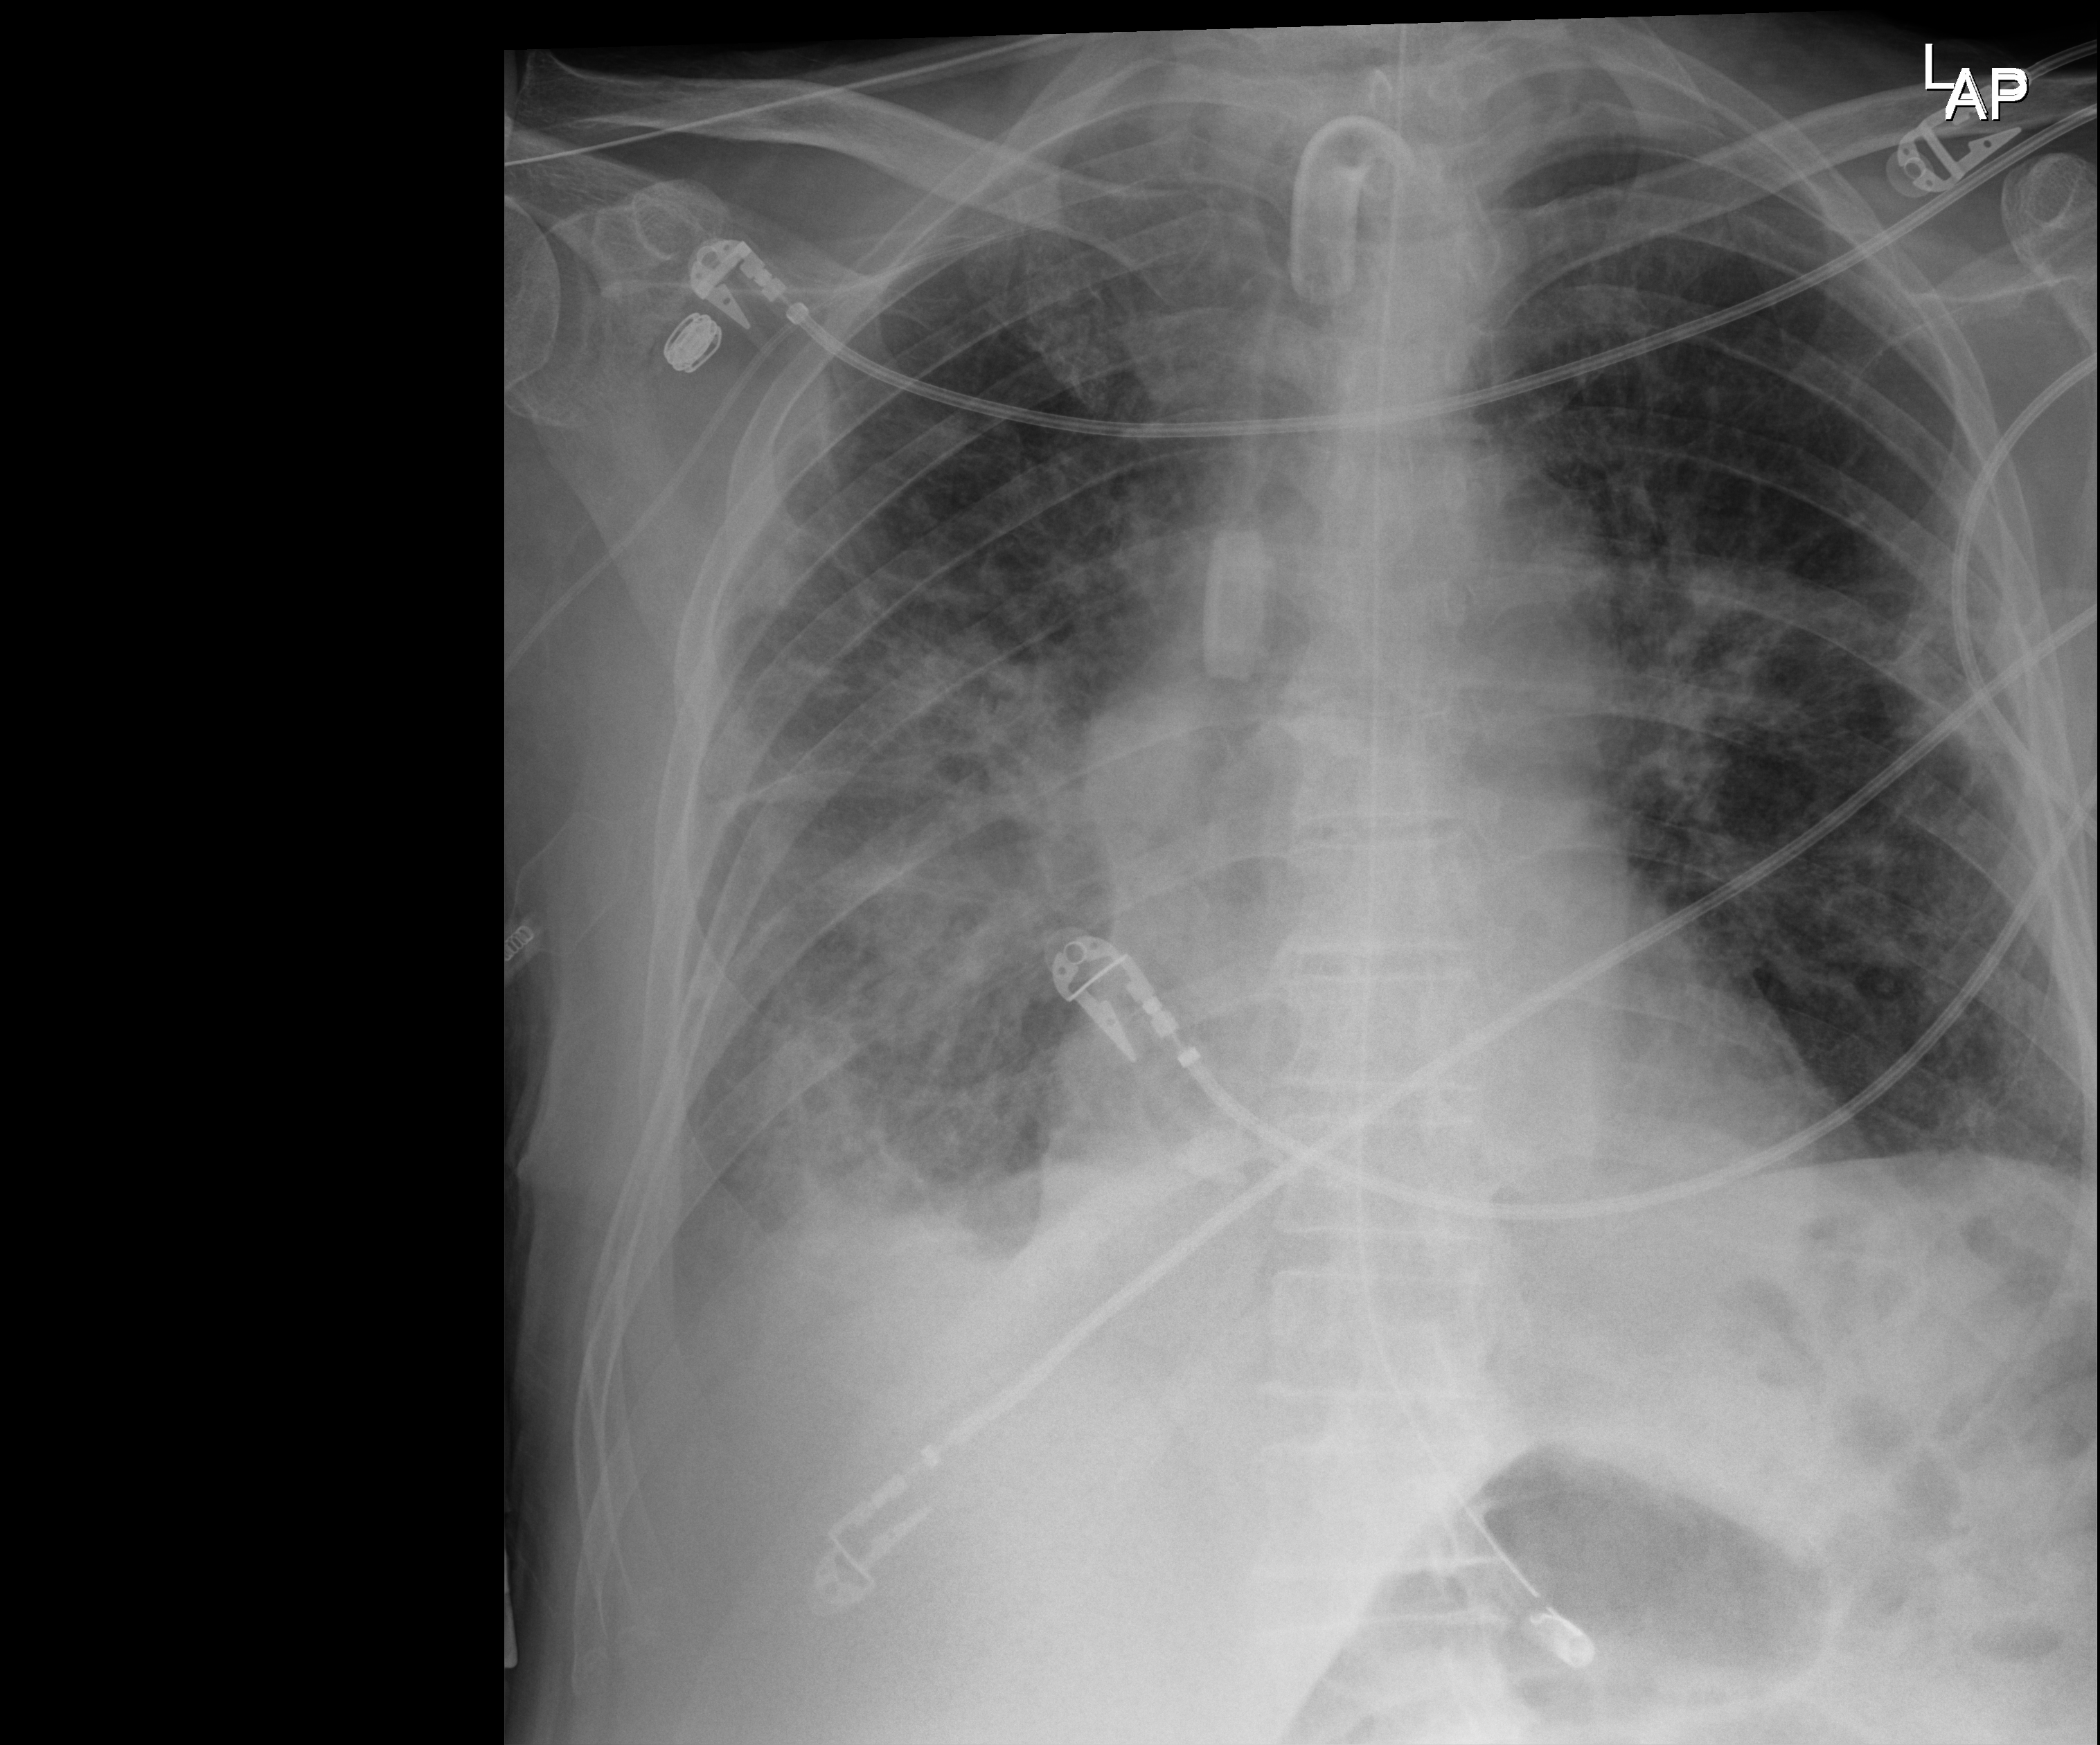
Bedside chest radiograph (digital radiography); anteroposterior (AP) projection. Male patient hospitalised with COVID-19, age 75–90 years.
From the hospital-stay record, not from the radiograph (when in the stay this image was taken is not recorded): COPD (admission record): no; other chronic lung disease (admission record): yes; admitted to intensive care during this hospital stay: yes.